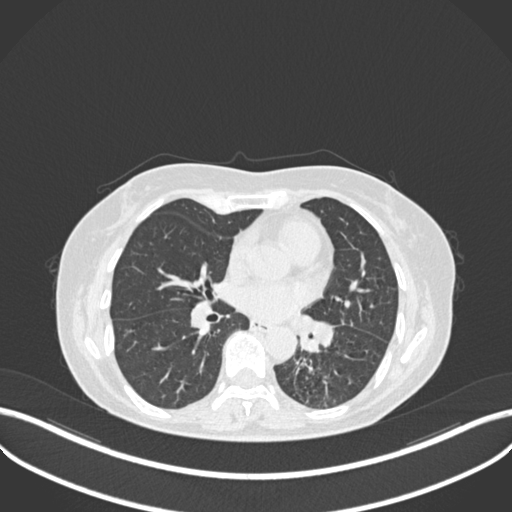
Chest CT, one axial slice. Slice 126 of 270 in the series (ordered by position). Reconstruction kernel B30f. 120 kVp. Lung window (W 1500 / L -600 HU). 1 mm slice thickness. 512 × 512 image matrix, field of view 400 × 400 mm. Female patient, age 63 years. Case-level facts recorded for this patient, not image findings: clinical TNM (as recorded): T1b N0 M0; histopathological grade: G2-3.
Outlined on this slice (rectangle marked by the reading radiologist):
- lung tumour (recorded histology: adenocarcinoma): box from (x=288, y=312) to (x=341, y=353) px